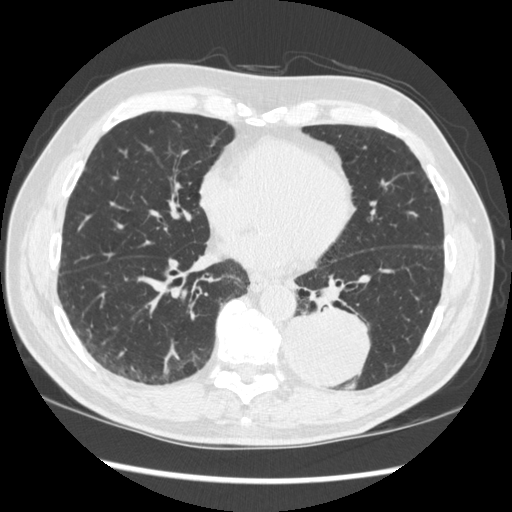
Low-dose screening chest CT, one axial slice; lung window (W 1500 / L -600 HU); 1.25 mm slice thickness; 512 × 512 image matrix.
Outlined on this slice (manually delineated by an expert):
- lesion 1 (tumor, lower lobe of left lung): bounding box (x1, y1, x2, y2) in pixels: (283, 309, 370, 389)